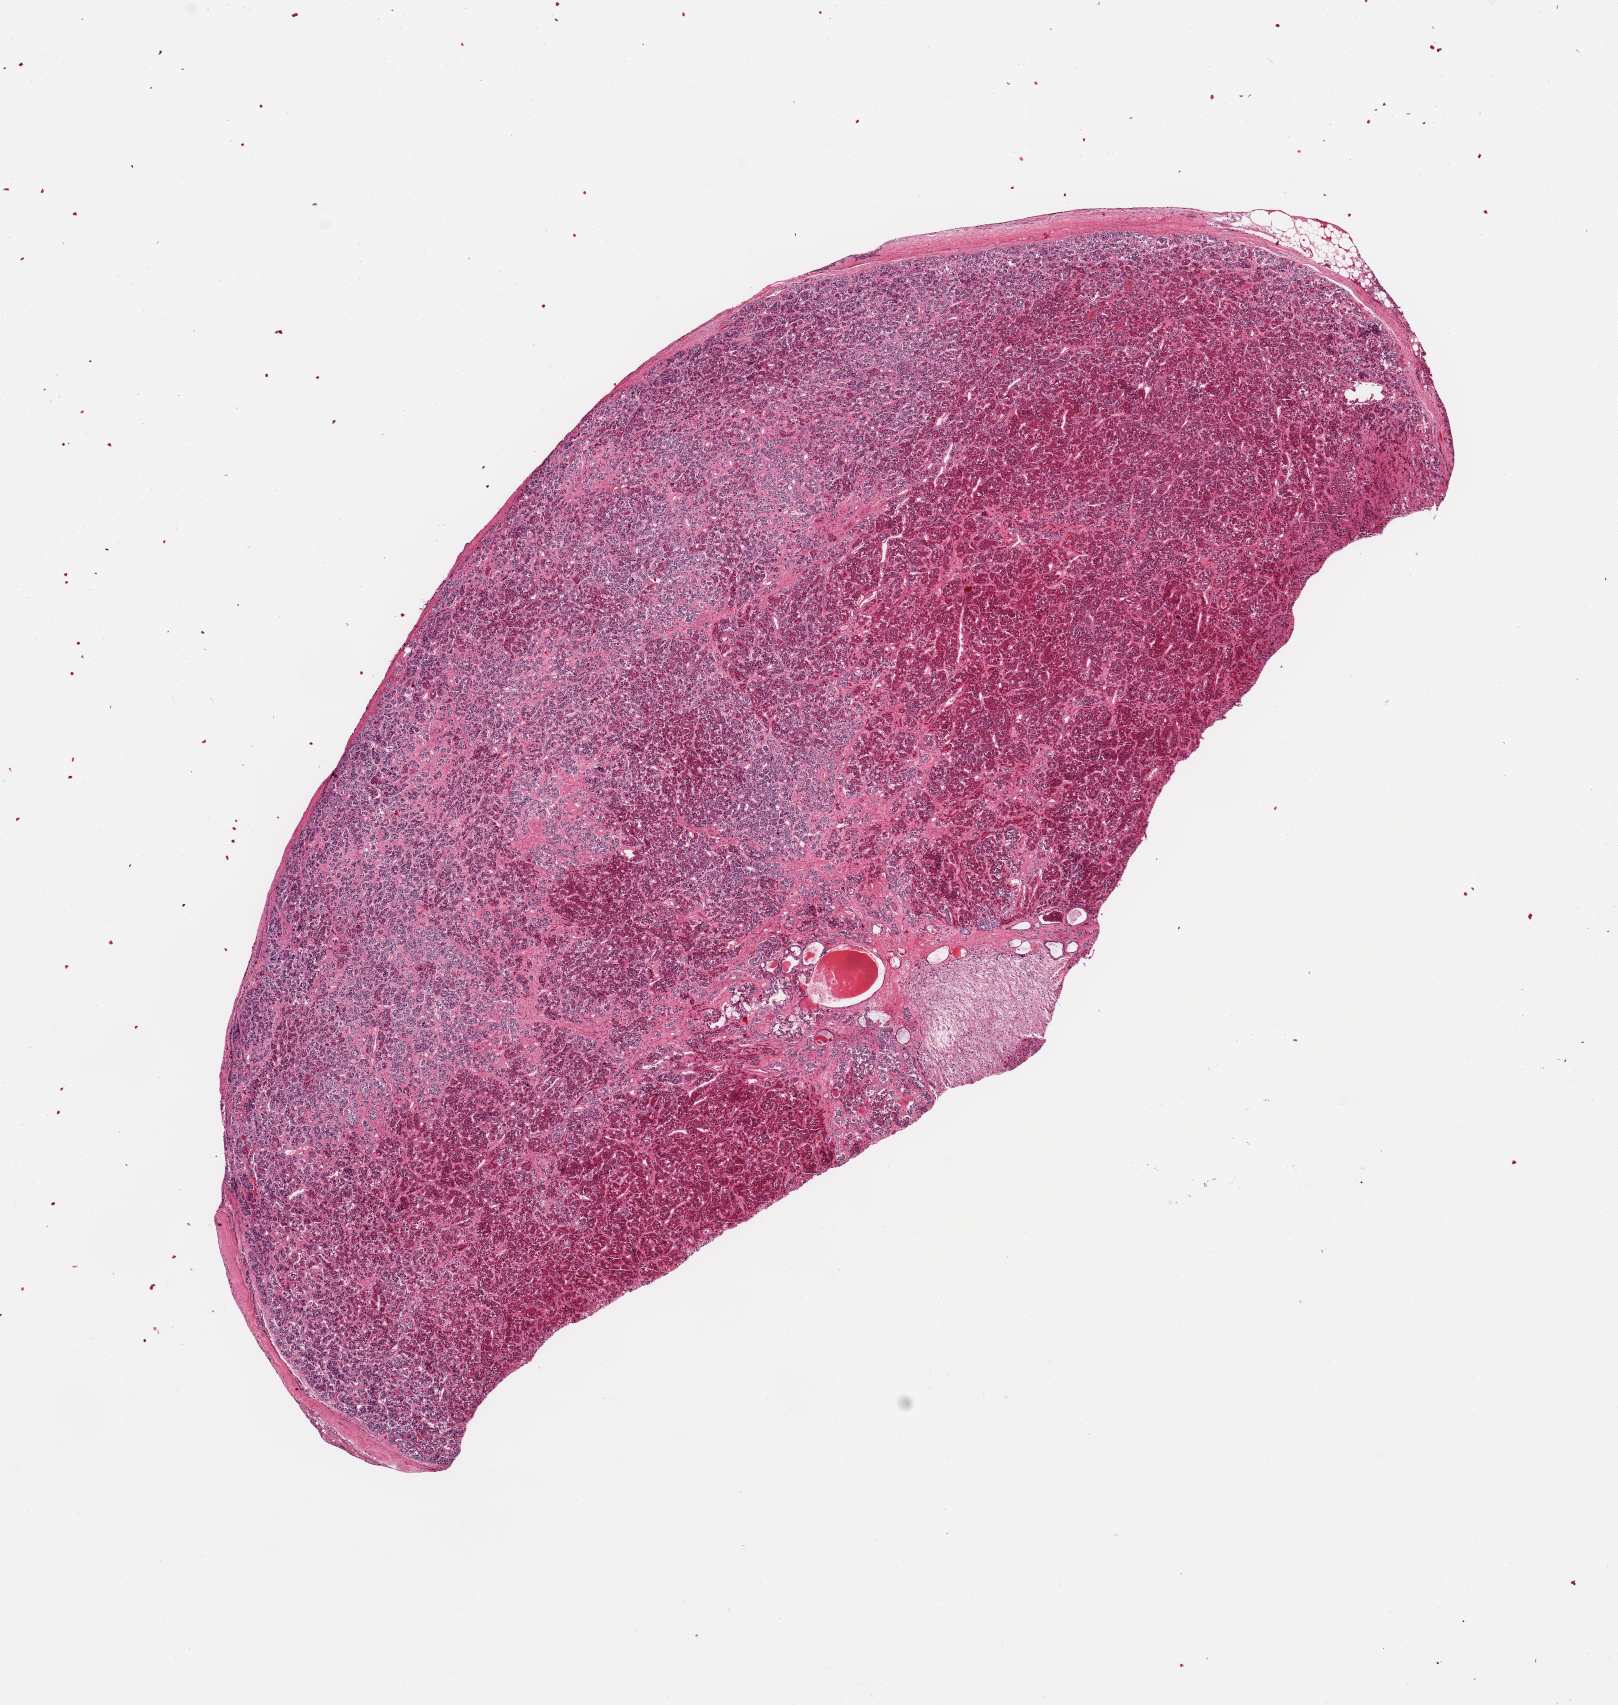
Haematoxylin and eosin whole-slide image, a low-resolution overview of the entire scanned area, about 12.8 x 13.5 mm (slide scanned at 20x). PAXgene-fixed, paraffin-embedded tissue. Target tissue: pituitary. Tissue donor sample. Donor: male.
Reviewer comment on this tissue sample: 1 piece; mostly anterior lobe; small posterior lobe.